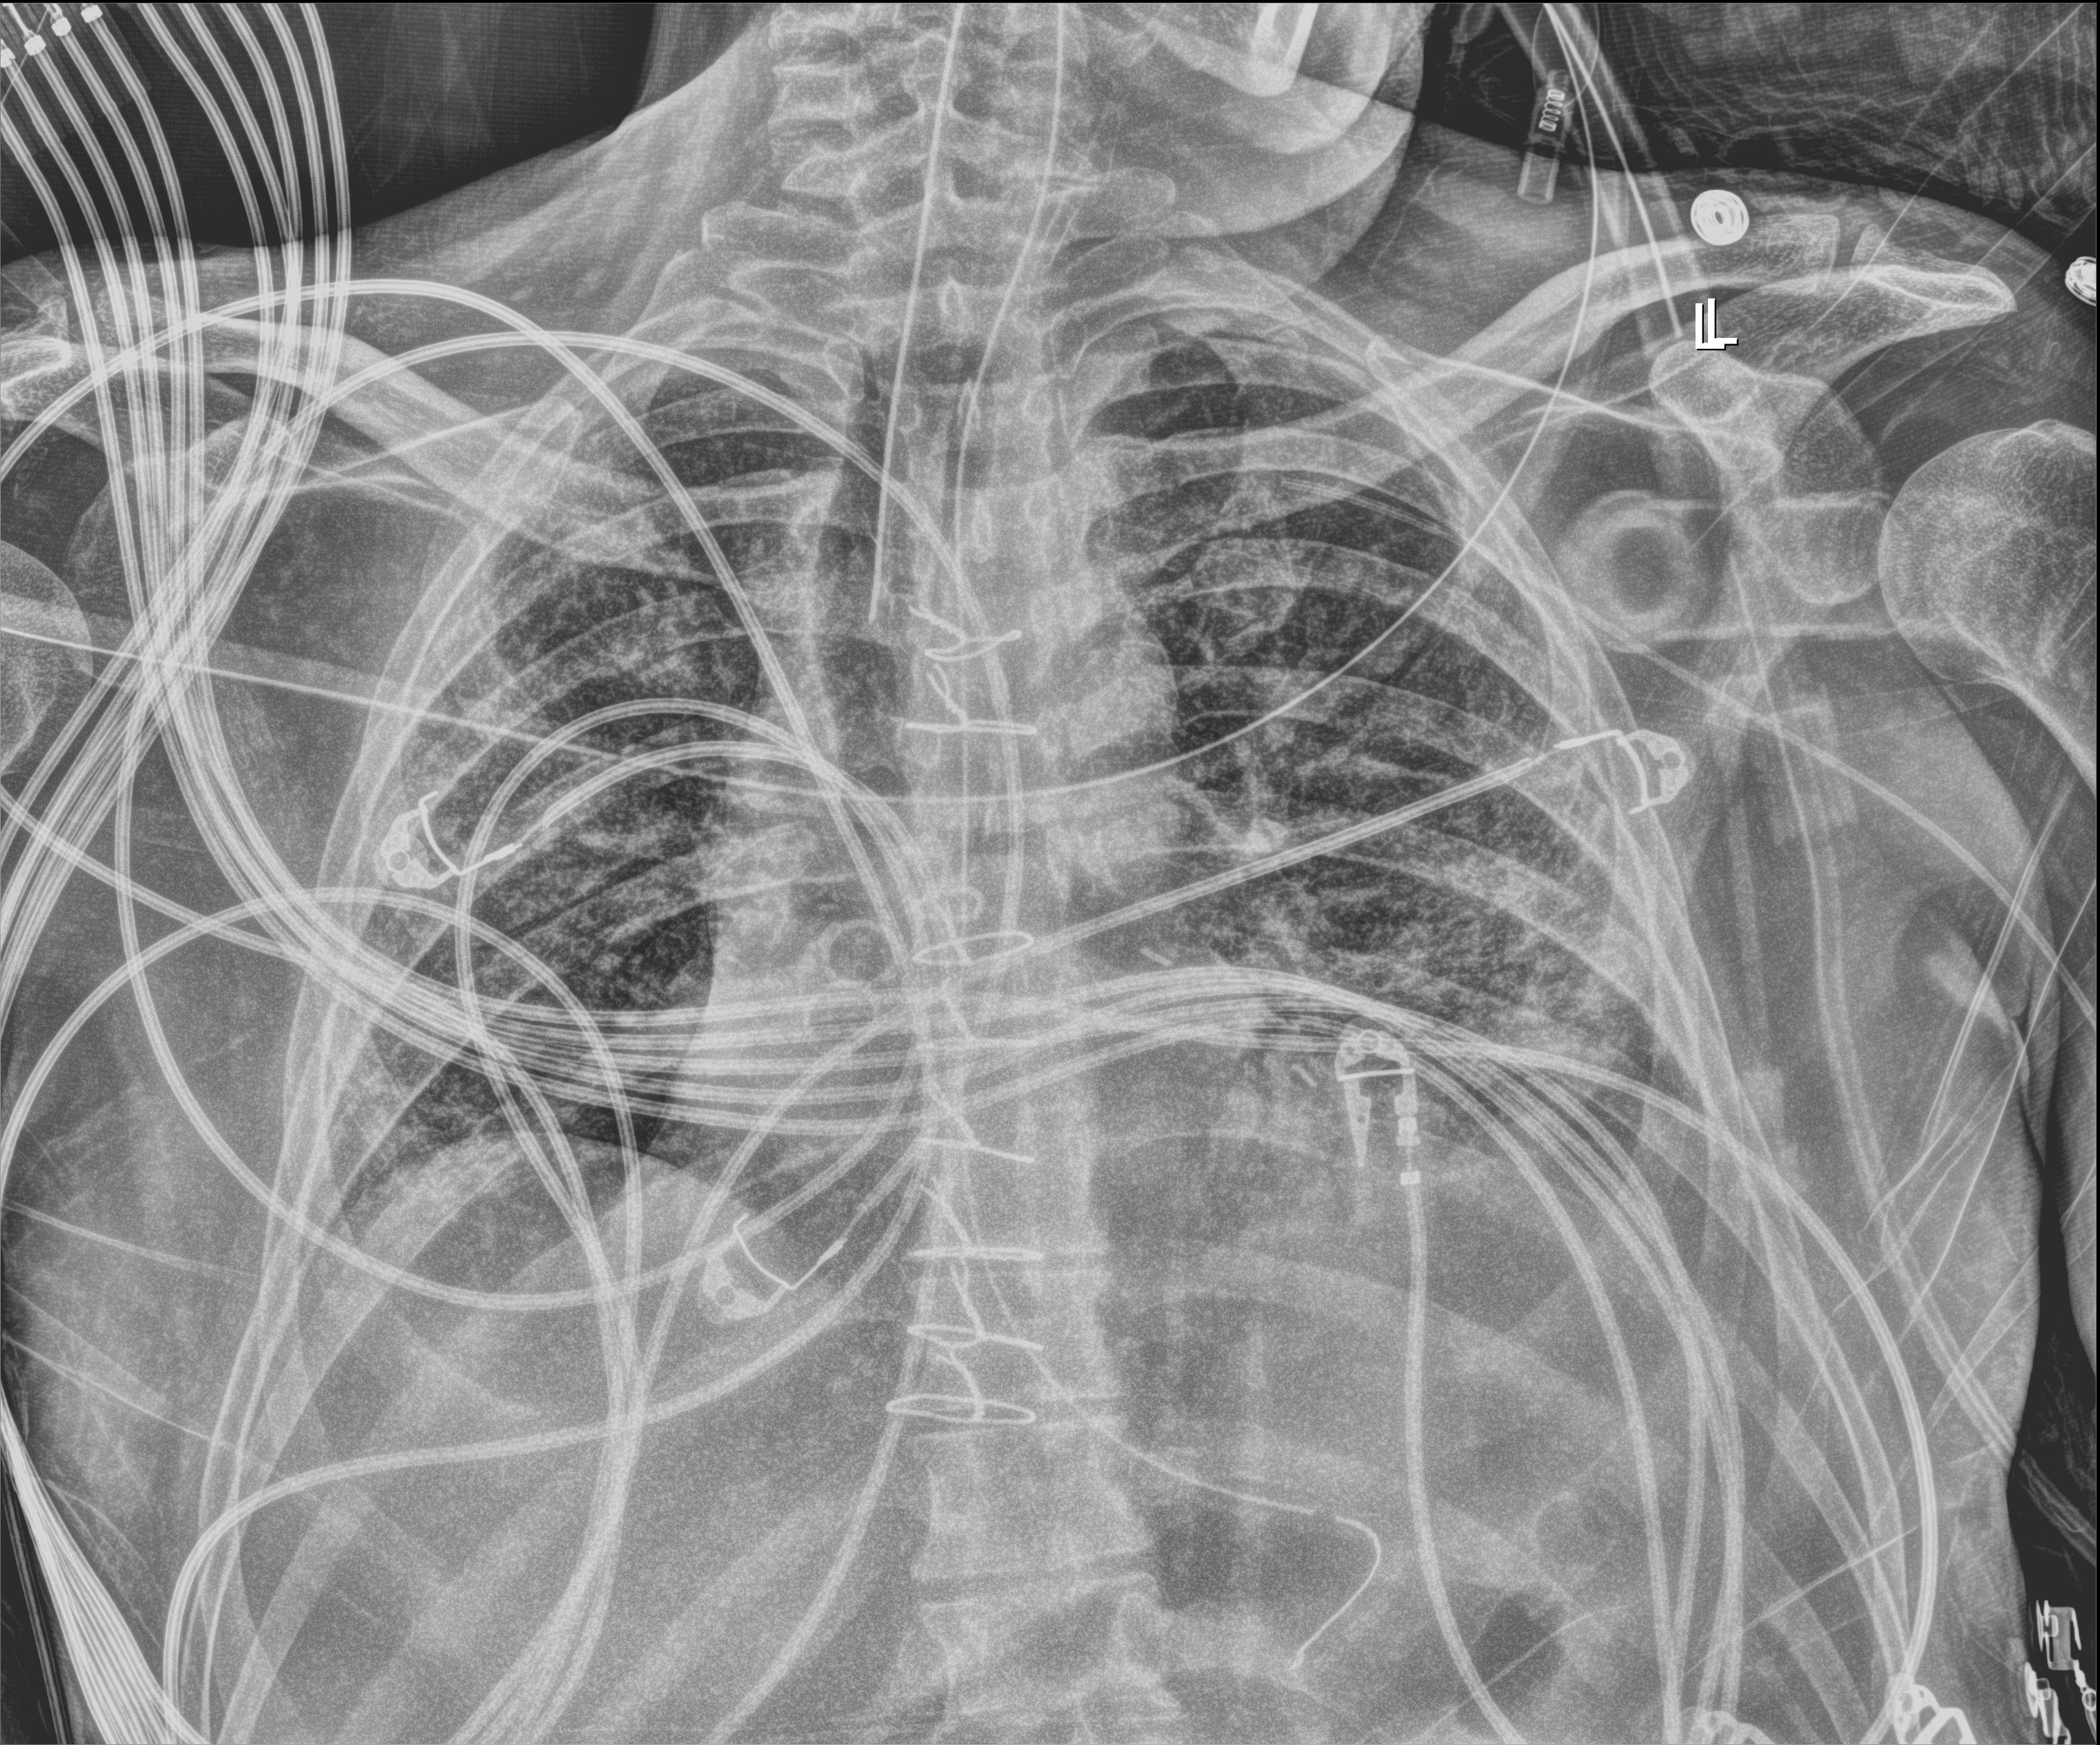
Bedside chest radiograph (digital radiography); anteroposterior (AP) projection. Male patient hospitalised with COVID-19, age 18–59 years.
Hospital-stay facts (about this admission, not read from this image; timing relative to this image not recorded):
- hypertension (admission record): no